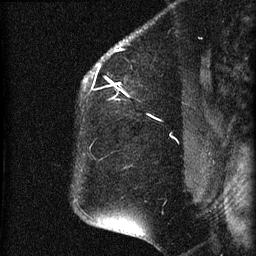
Breast MRI (dynamic contrast-enhanced), one sagittal slice; slice 52 of 60 in the series (ordered by position); dynamic contrast-enhanced series, image 2 of 4 at this slice position (ordered by acquisition); 1.5 T; TE 4.2 ms, TR 22.7 ms; 1.5 mm slice thickness; 256 × 256 image matrix, field of view 180 × 180 mm. Patient: female, 35 years. From the clinical record (not read from this slice): setting: breast cancer imaged before/during neoadjuvant chemotherapy; receptor status: HR-positive, HER2-negative.
Annotated regions visible in this slice (semi-automatically segmented with operator editing):
- analysis volume of interest (the breast-tissue region the enhancement analysis was run in; not a lesion): bounding box (x1, y1, x2, y2) in pixels: (75, 27, 199, 112)
- tumour enhancement mask (voxels above the 90 % enhancement threshold inside the analysis volume of interest): (84, 49, 129, 100)